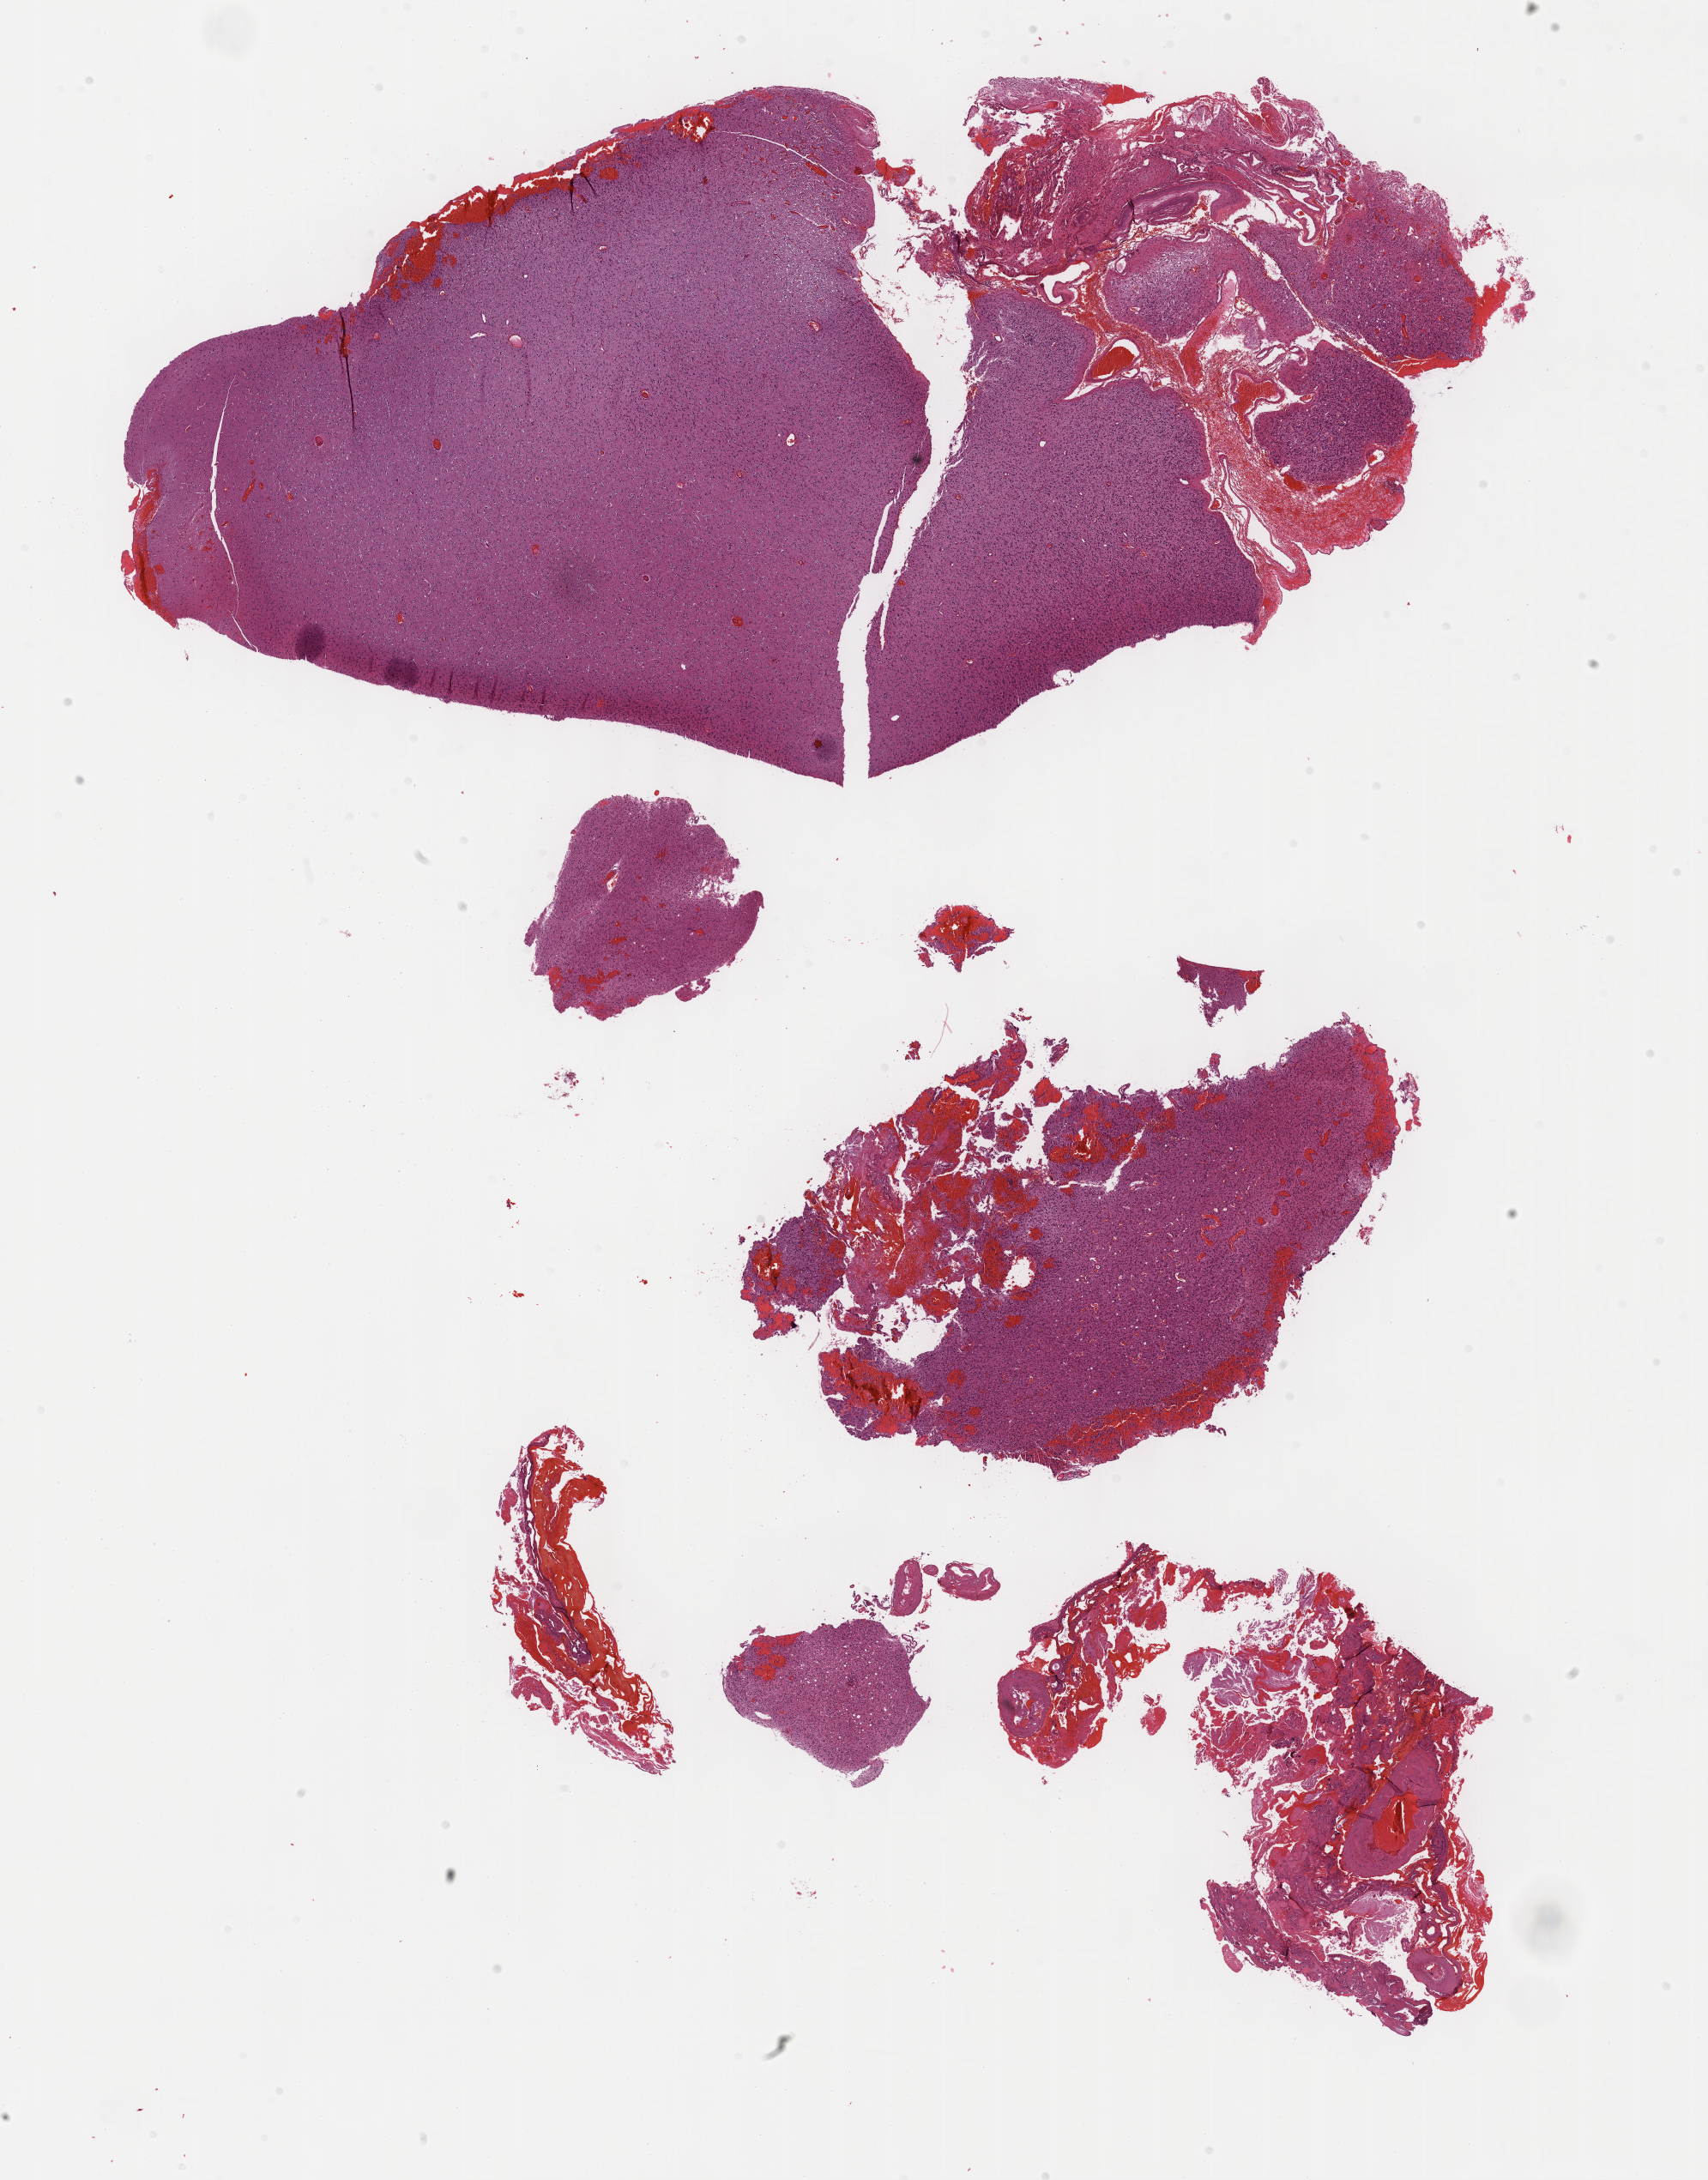
Whole-slide histology image, H&E — whole scanned area (about 16.1 x 20.6 mm) shown as a low-resolution overview. FFPE section. Sample: primary tumour, brain. Male, age 14 years at initial diagnosis. Histologic grade: G2 (moderately differentiated).
Pathologic diagnosis: Mixed glioma (cerebrum).